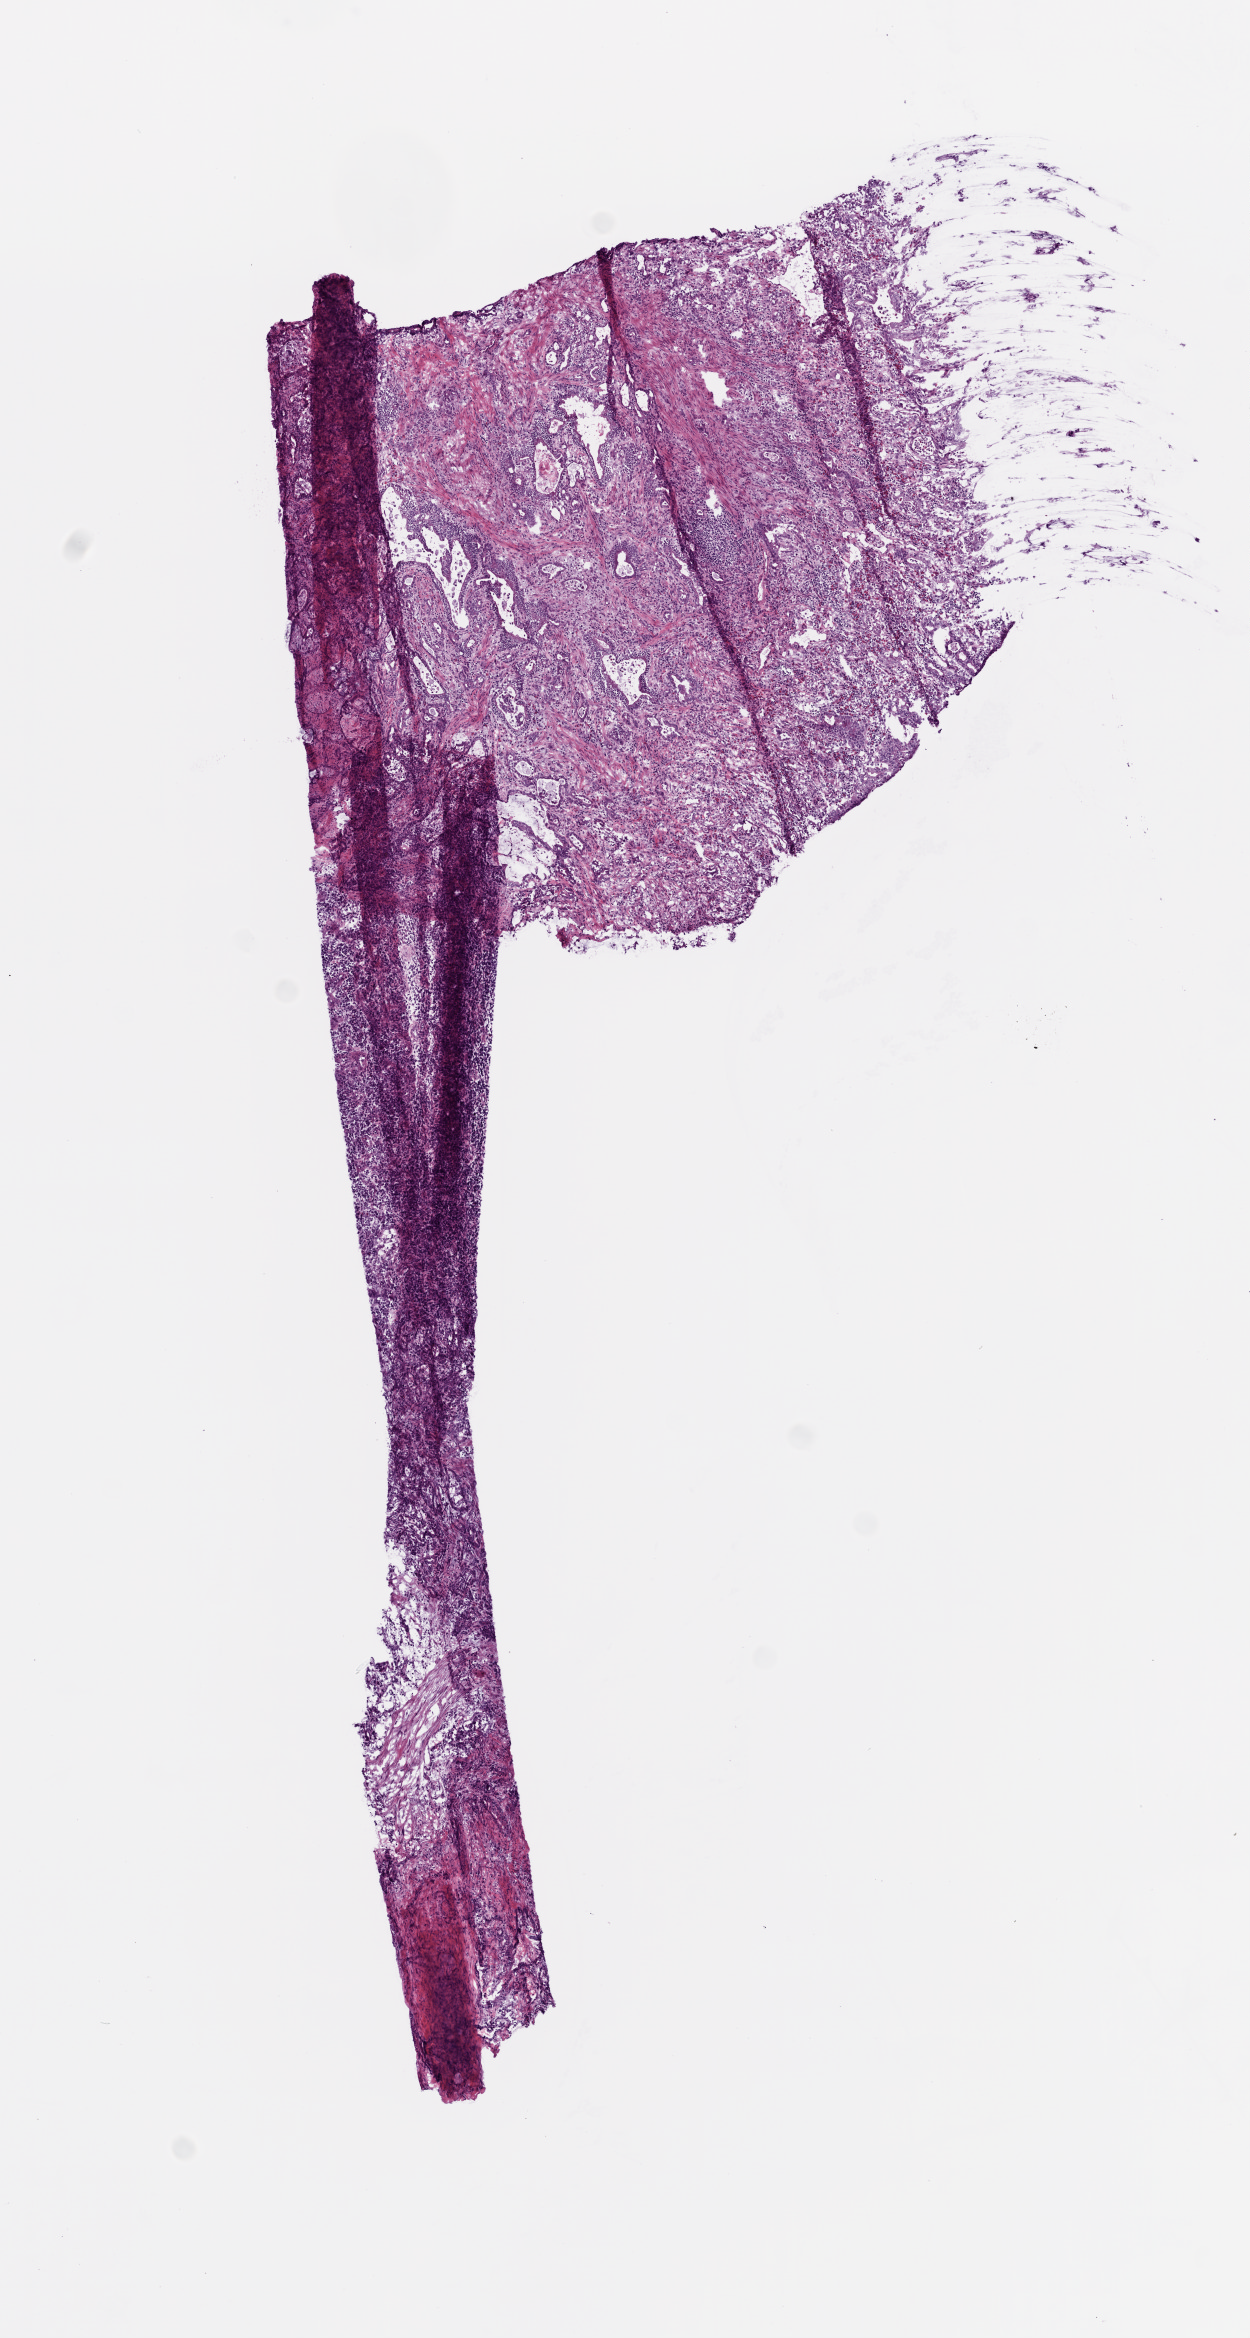
Hematoxylin and eosin (H&E) stained whole-slide image — a low-resolution overview of the entire scanned area, about 5.0 x 9.4 mm (acquisition: 20x scan). Frozen section. Stomach, primary tumour sample. Patient: female, age at initial diagnosis 54 years. Histologic grade: G1 (well differentiated). Slide review estimates, as recorded: tumour cells 75%, tumour nuclei 70%, normal cells 0%, stromal cells 25%, necrosis 0%.
• lymph nodes positive (case pathology): 0 of 15 examined
• diagnosis: Adenocarcinoma, intestinal type (body of stomach)
• AJCC pathologic stage: IV (7th edition)